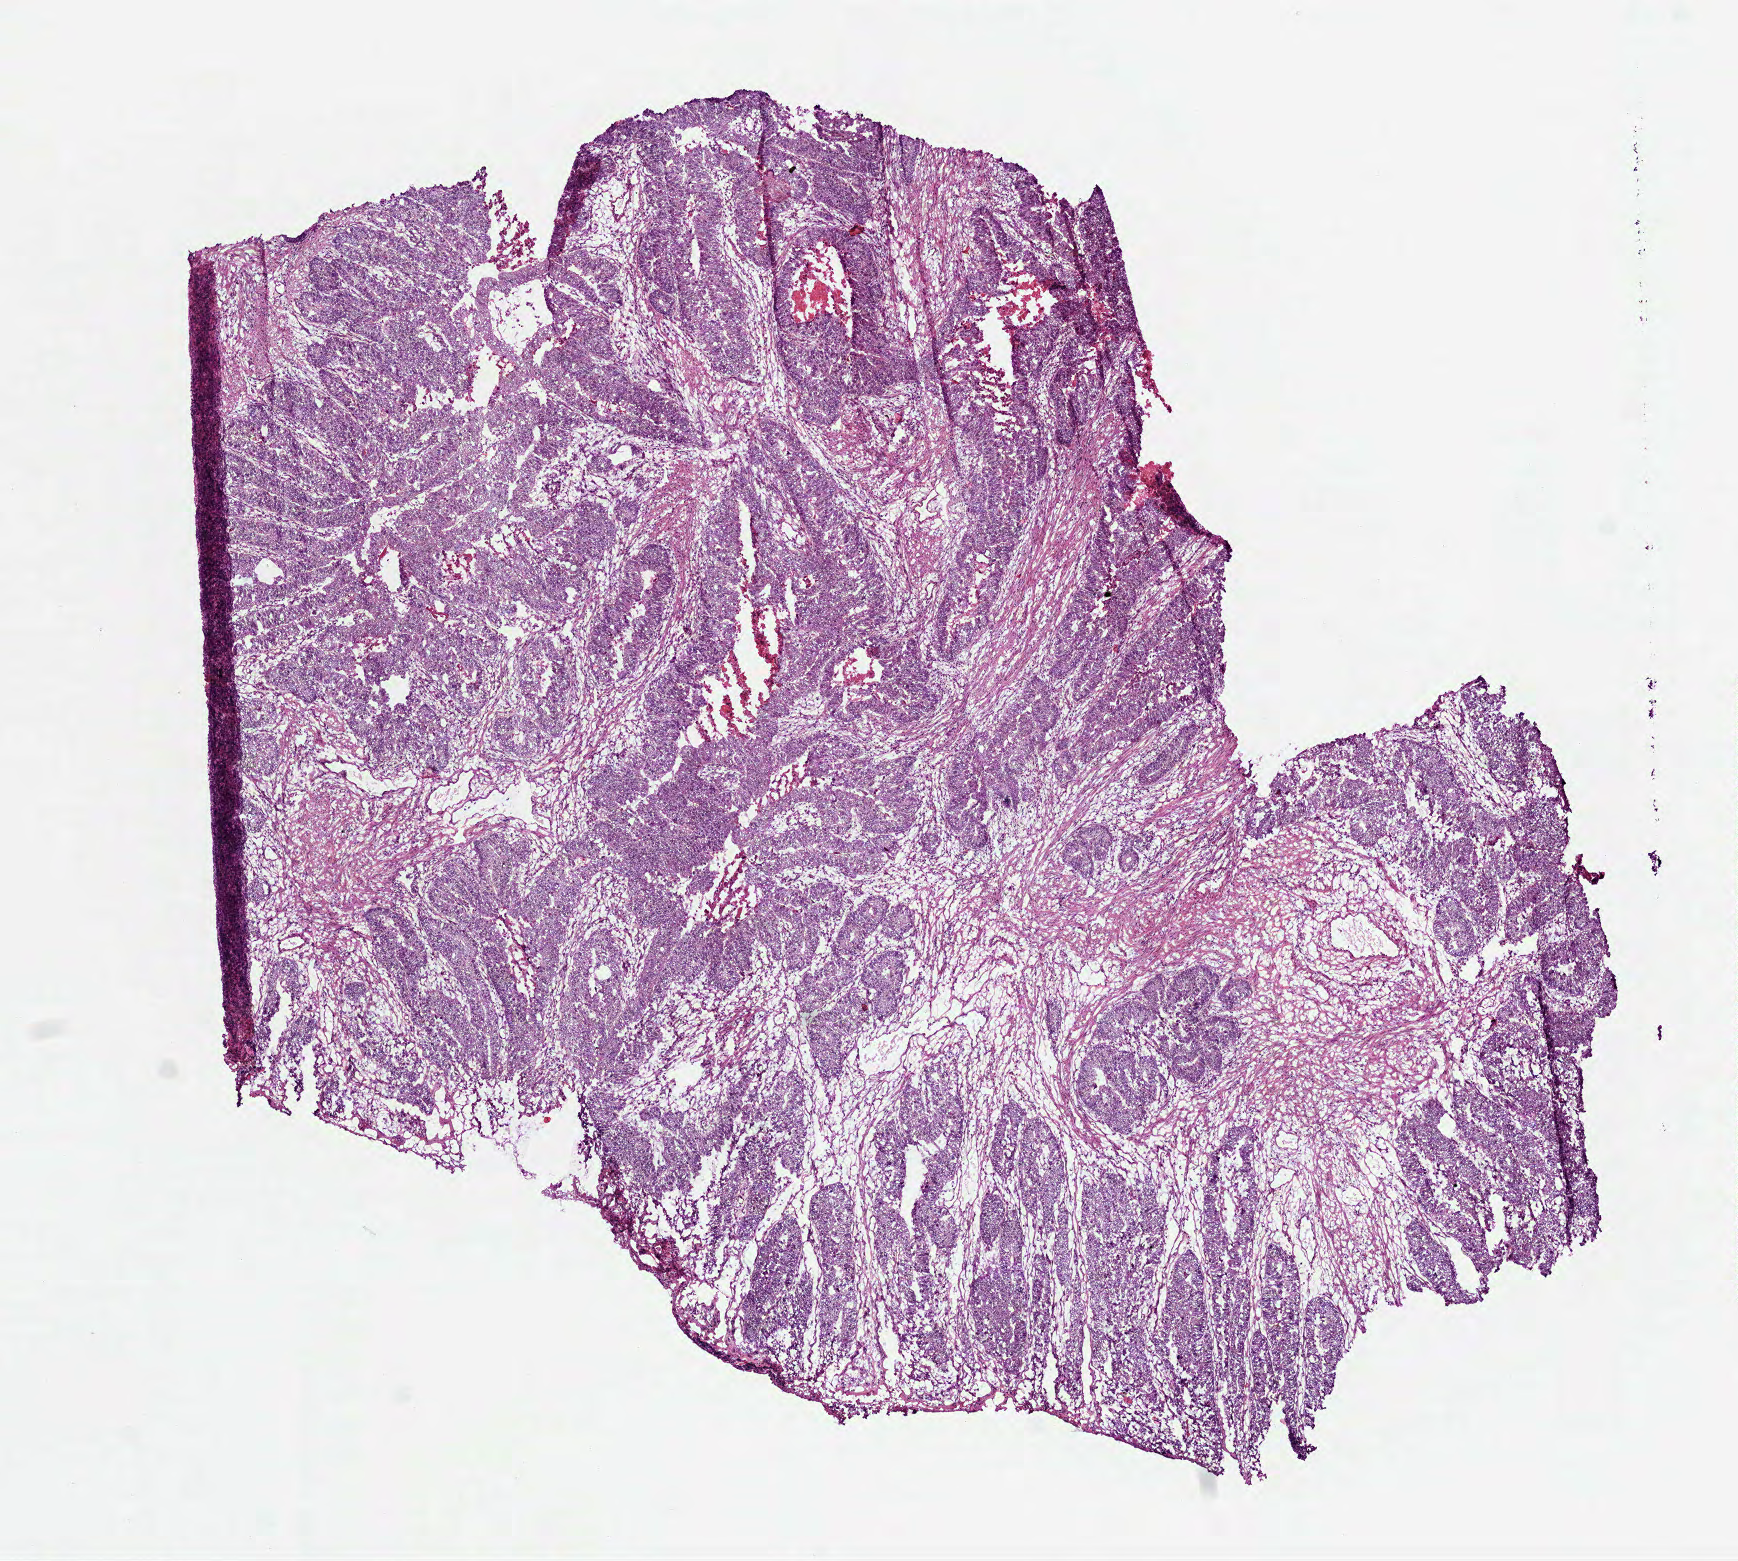
Whole-slide histology image, Hematoxylin and eosin (H&E) stained — whole scanned area (about 7.0 x 6.3 mm, slide scanned at 40x) shown as a low-resolution overview; frozen section from the top of the tissue portion; sample: primary tumour, rectum. Patient: male, age at initial diagnosis 66 years. Pathologist review of this section (percent, as recorded): tumour cells 77%, tumour nuclei 80%, normal cells 0%, stromal cells 15%, necrosis 8%.
• histologic diagnosis: Adenocarcinoma, NOS